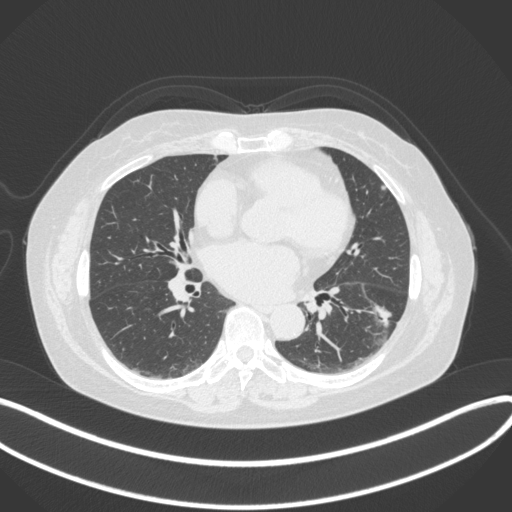
Chest CT, one axial slice; slice 168 of 373 in the series (ordered by position); reconstruction kernel B31f; 120 kVp; lung window (W 1500 / L -600 HU); 1 mm slice thickness; 512 × 512 image matrix, field of view 400 × 400 mm. Patient: female, 67 years. Case-level facts recorded for this patient, not image findings: clinical TNM (as recorded): T1c N0 M0.
Outlined on this slice (bounding box drawn by a radiologist):
- lung tumour (recorded histology: adenocarcinoma): box from (x=362, y=296) to (x=398, y=332) px